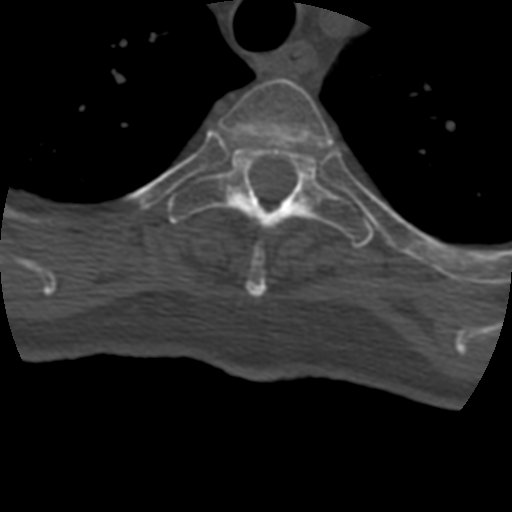
CT including the spine, one axial slice; position 342 of 399 along the scan axis; reconstruction kernel STANDARD; bone window (W 1800 / L 400 HU); 1.25 mm slice thickness; 512 × 512 image matrix, field of view 160 × 160 mm. Patient age 69 years. From the clinical record (not read from this slice): primary cancer: prostate.
Annotated regions visible in this slice (semi-automatic segmentation, software-assisted and operator-edited):
- T3 vertebra: bounding box [x1, y1, x2, y2] px = [220, 79, 332, 298]
- T4 vertebra: [169, 144, 375, 248]